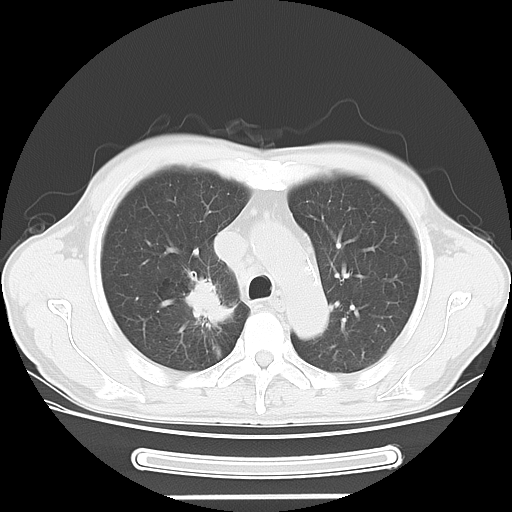
Chest CT, one axial slice. Slice 36 of 51 in the series (ordered by position). 120 kVp. Lung window (W 1500 / L -600 HU). 5 mm slice thickness. 512 × 512 image matrix, field of view 350 × 350 mm. Patient: male, 57 years. From the clinical record (not read from this slice): clinical TNM (as recorded): T2 N3 M1b.
Structures marked on this image (bounding box drawn by a radiologist):
- lung tumour (recorded histology: adenocarcinoma): bounding box [x1, y1, x2, y2] px = [184, 271, 232, 332]